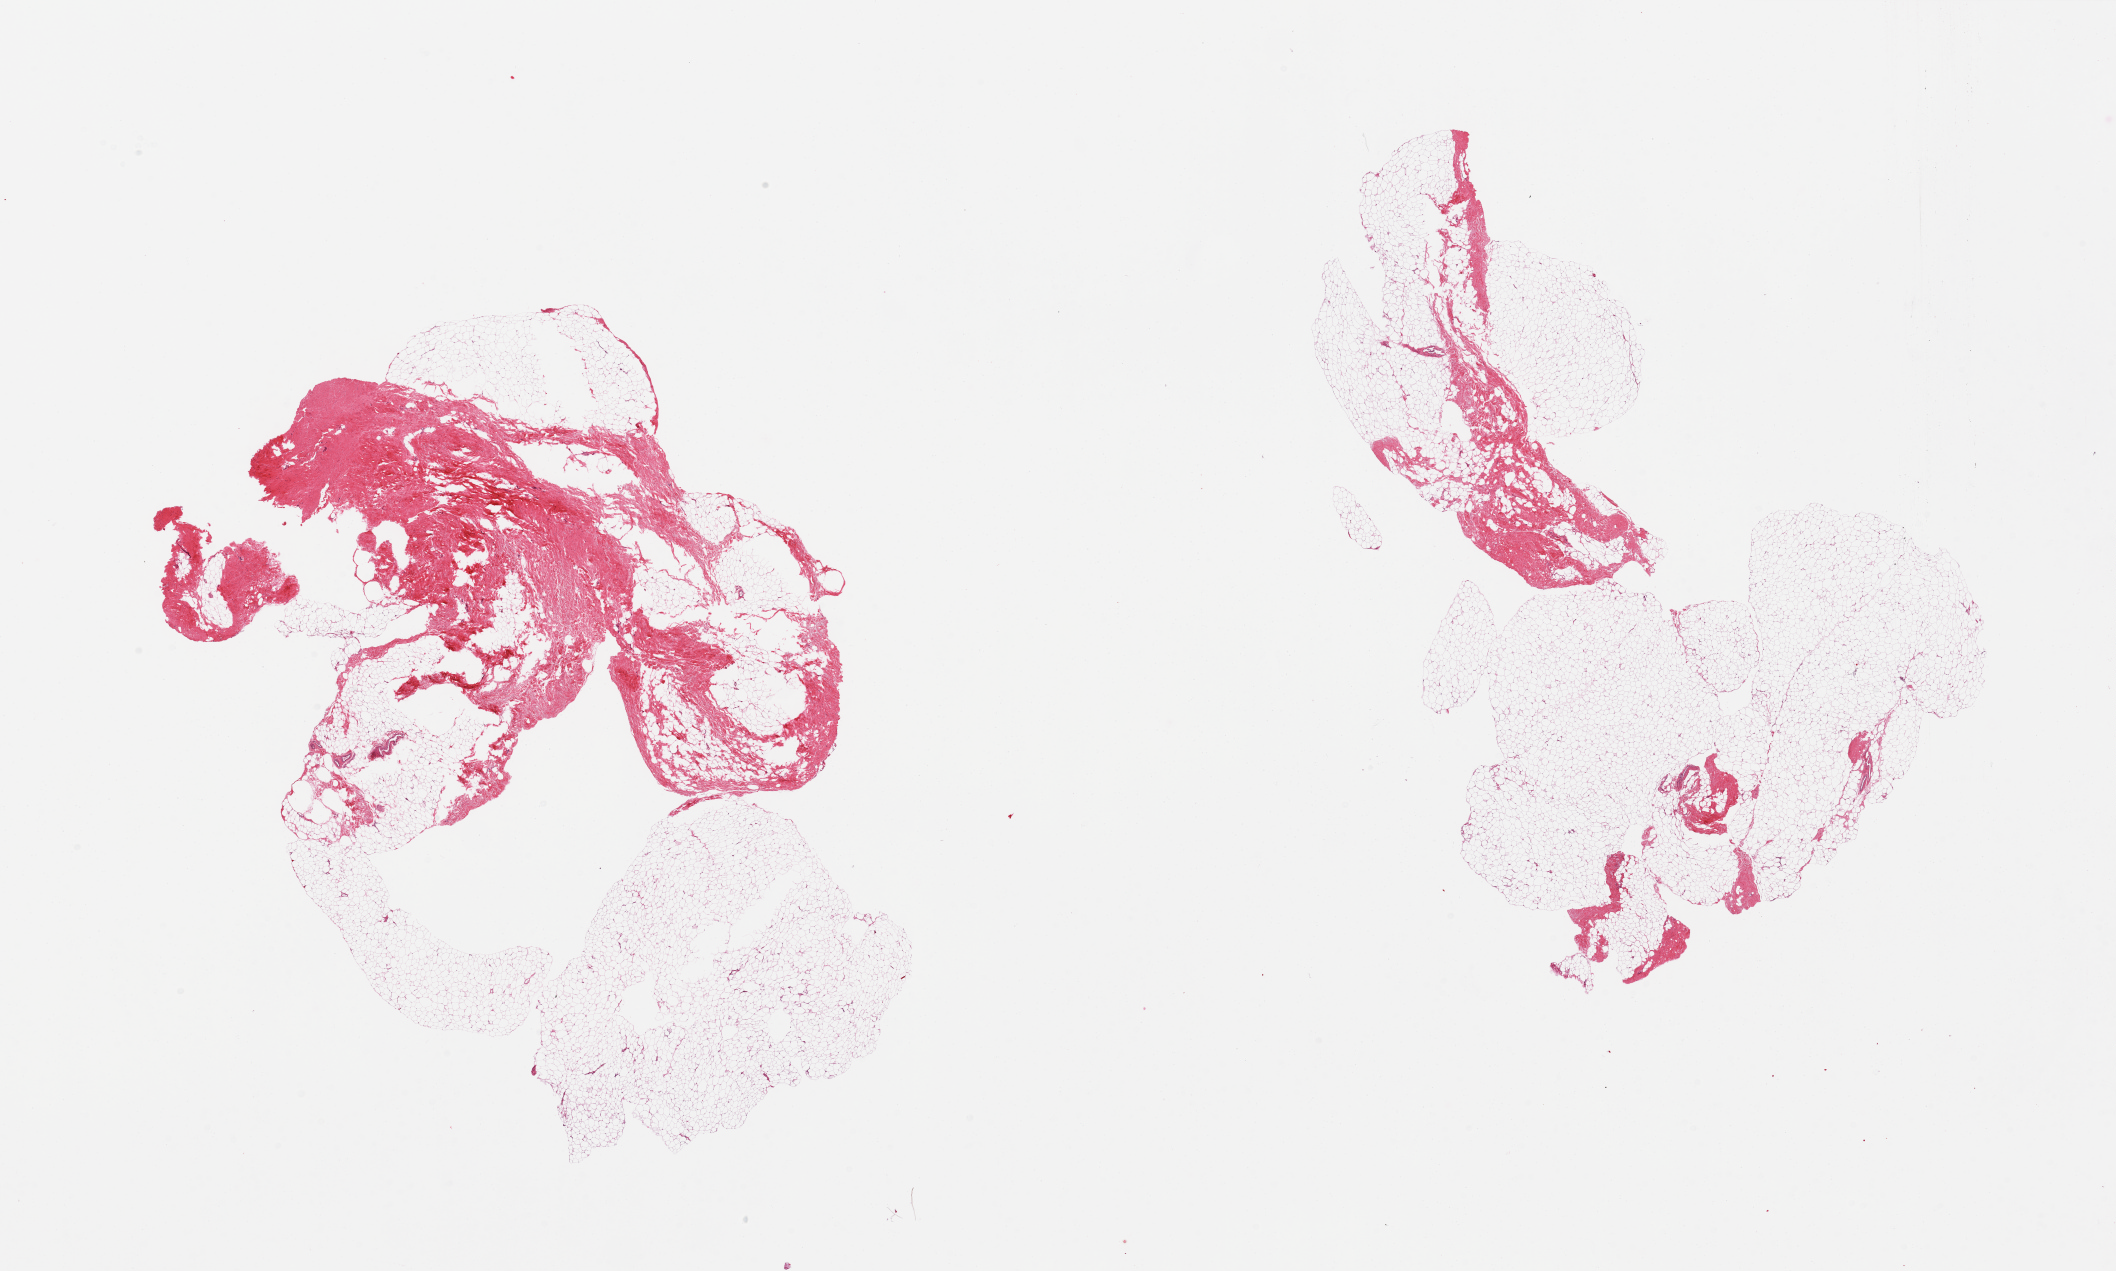
Haematoxylin and eosin whole-slide image — a low-resolution overview of the entire scanned area, about 33.5 x 20.1 mm, PAXgene-fixed paraffin-embedded (PFPE) section, target tissue: breast, tissue donor sample. Donor: male.
* reviewer comment on this tissue sample: 2 pieces, one is ~20% fibrous stroma, second is ~50% fibrous, no ductal epithelium identiifed